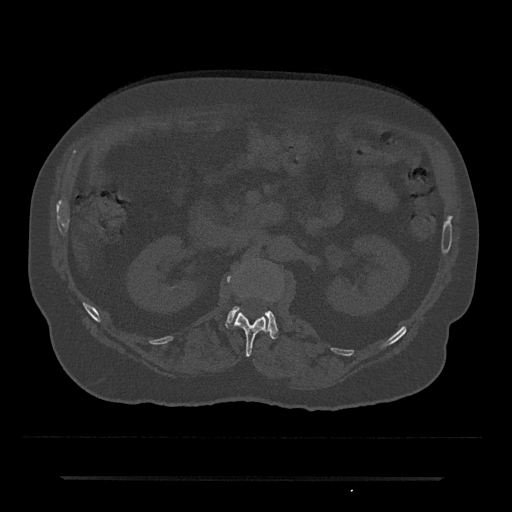
CT including the spine, one axial slice. Slice 45 of 797 in the series (ordered by position). Bone window (W 1800 / L 400 HU). 512 × 512 image matrix. Patient: male, 69 years. From the clinical record (not read from this slice): primary cancer: prostate.
Annotated regions visible in this slice (semi-automatically segmented with operator editing):
- L1 vertebra: bounding box (x1, y1, x2, y2) in pixels: (227, 276, 267, 357)
- L2 vertebra: (227, 306, 278, 339)